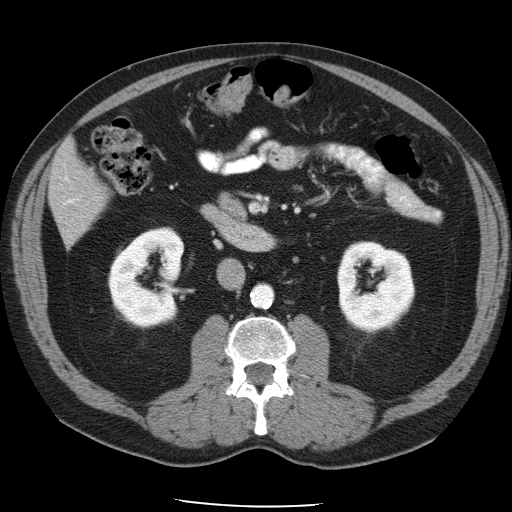
Contrast-enhanced abdominal CT, one axial slice; reconstruction kernel STANDARD; intravenous contrast given; soft-tissue window (W 400 / L 40 HU); 512 × 512 image matrix, field of view 395 × 395 mm. Male patient, age 68 years. Case-level facts recorded for this patient, not image findings: diagnosis: colorectal cancer liver metastases, imaged before liver resection; multiple liver metastases: yes; largest metastasis: 1.7 cm; chemotherapy before resection: yes.
Outlined on this slice (manually delineated by an expert):
- liver: bounding box (x1, y1, x2, y2) in pixels: (50, 141, 107, 242)
- planned liver remnant (the part of the liver to remain after resection): (62, 141, 79, 165)
- portal vein (with intrahepatic branches): (65, 177, 80, 205)